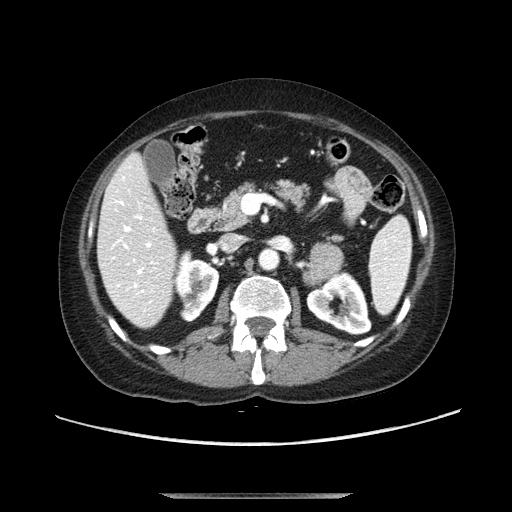
Contrast-enhanced abdominal CT, one axial slice; position 54 of 107 along the scan axis; soft-tissue window (W 400 / L 40 HU); 2.5 mm slice thickness; 512 × 512 image matrix. Female patient. From the clinical record (not read from this slice): diagnosis: adrenocortical carcinoma; tumour side: left adrenal; tumour size at pathology: 7.5 cm; Ki-67 index: 9 %.
Structures marked on this image (semi-automatically segmented with operator editing):
- mass: bounding box (x1, y1, x2, y2) in pixels: (304, 242, 345, 286)